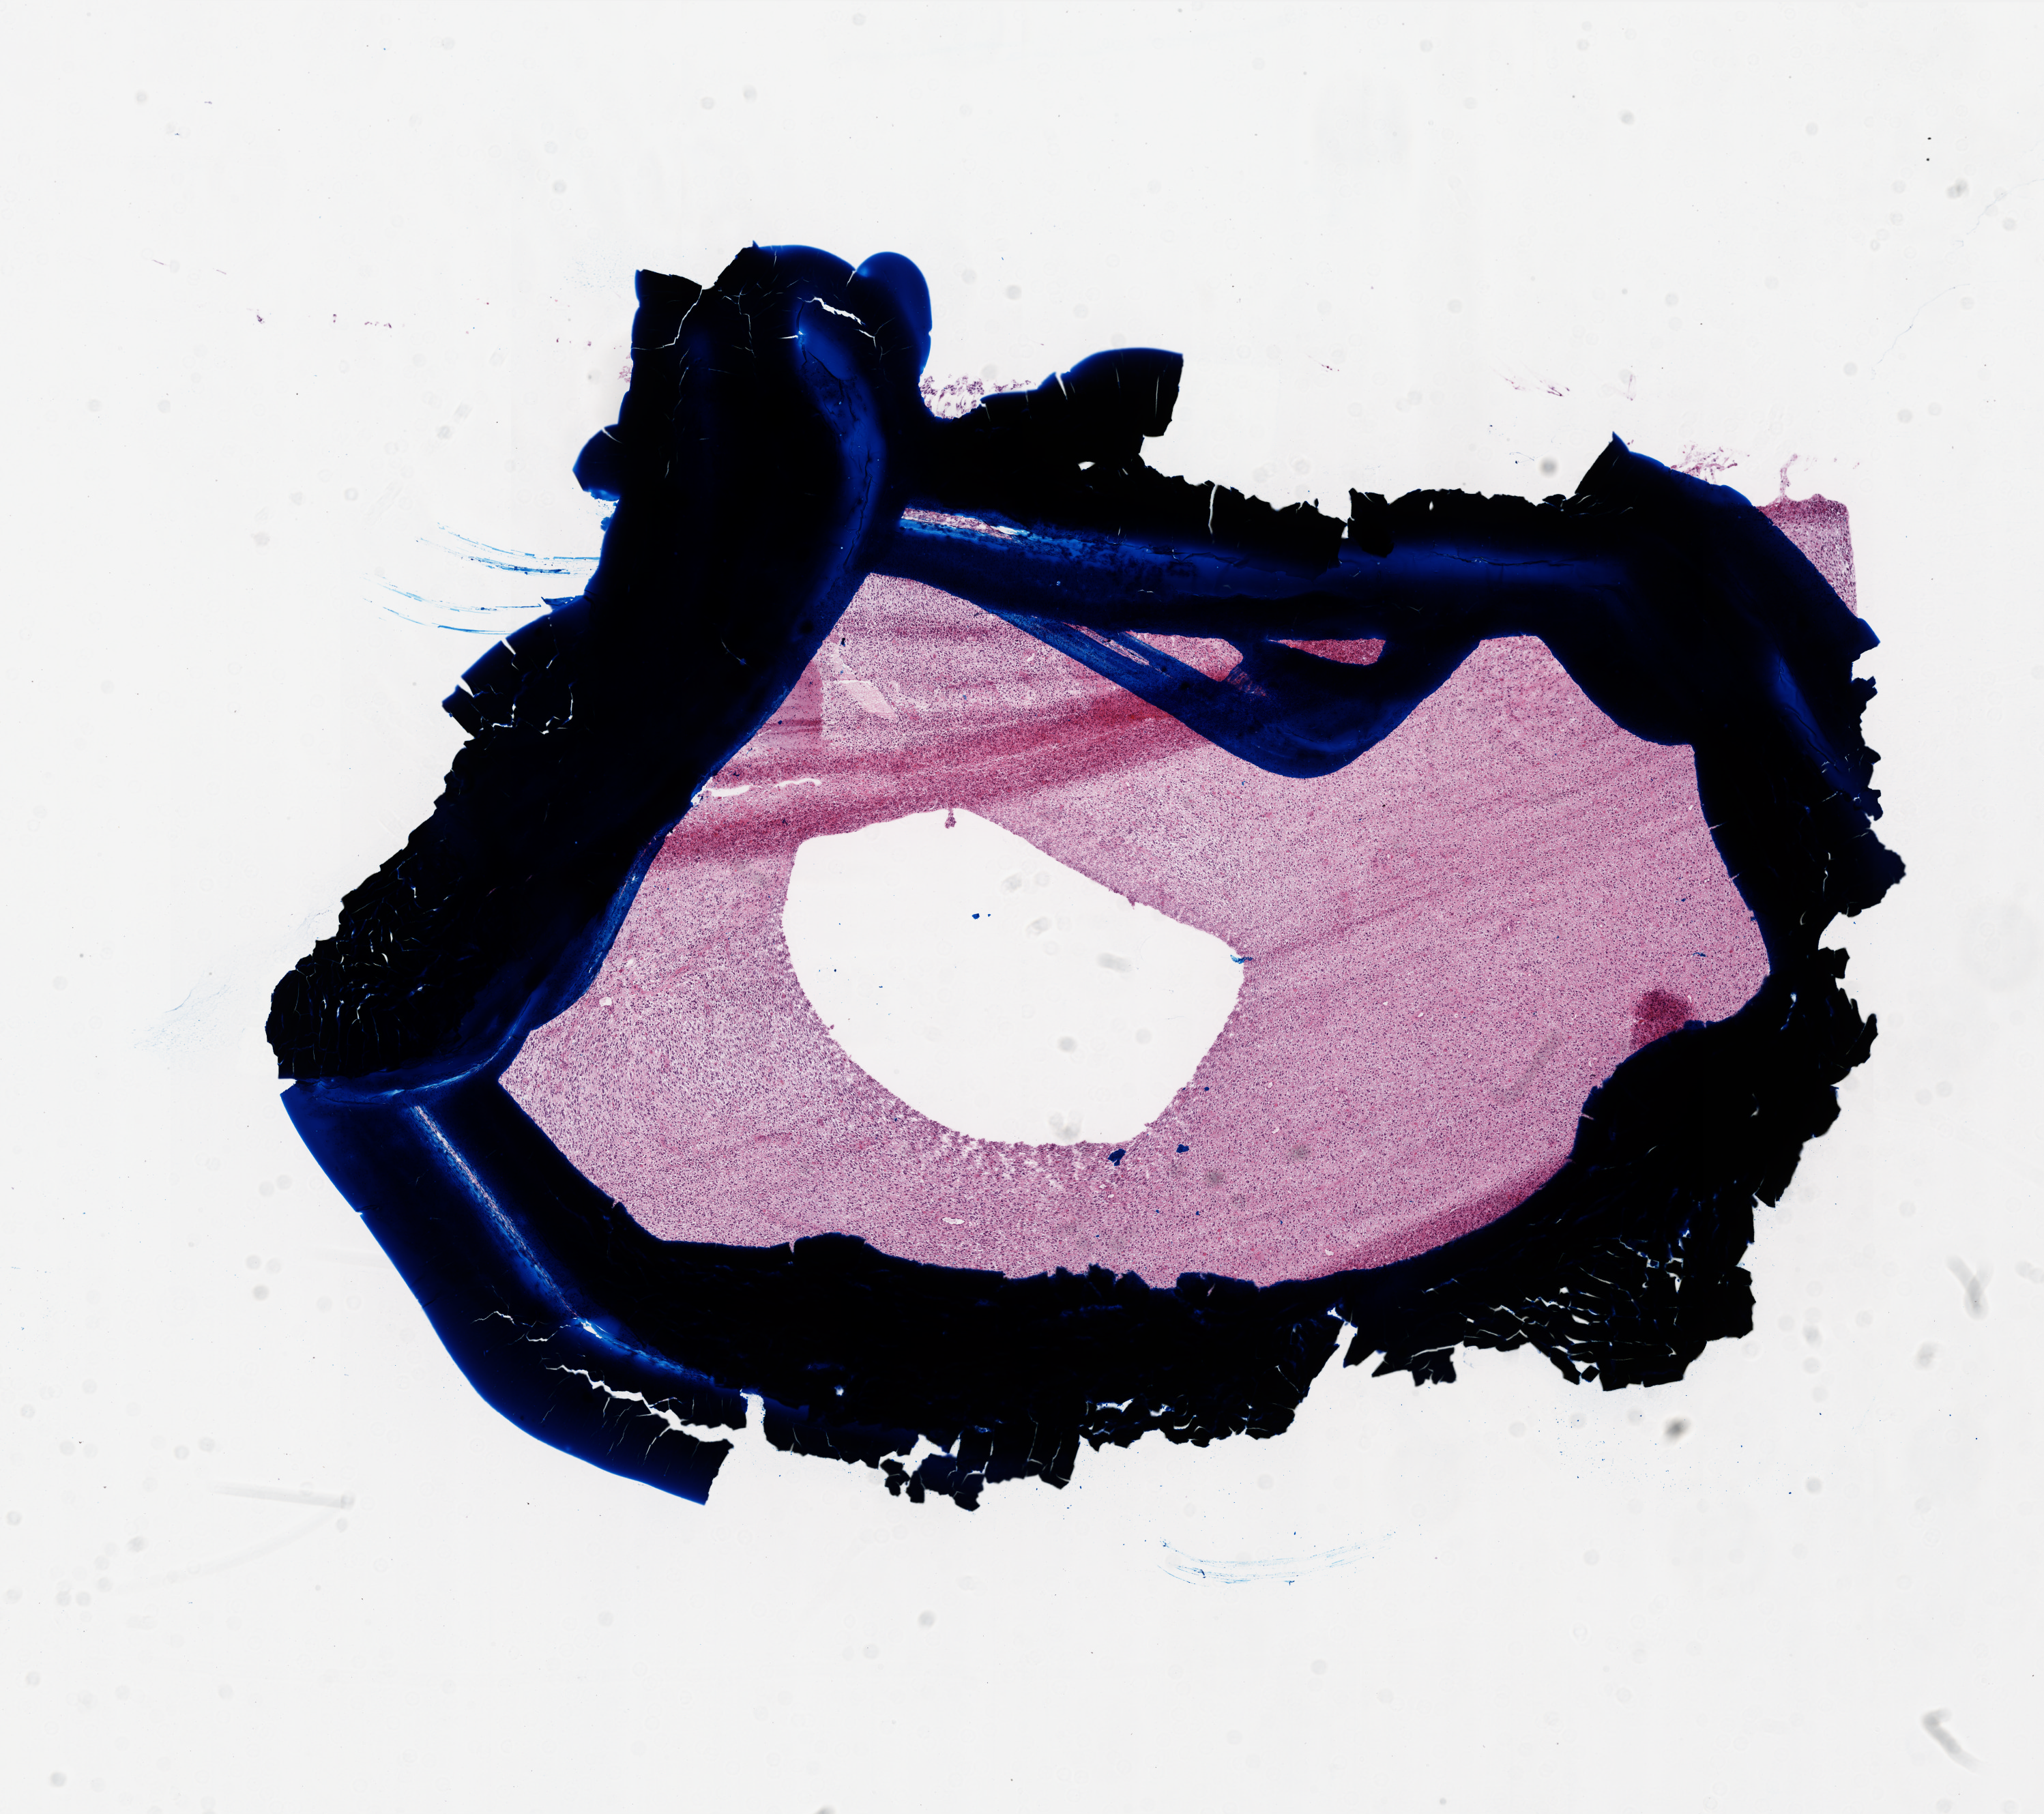
Digitized Hematoxylin and eosin (H&E) stained tissue section (whole slide), shown as a low-resolution overview of the whole scanned area (about 12.0 x 10.6 mm). Frozen section from the top of the tissue portion. Sample: primary tumour, brain. Patient: male, age at initial diagnosis 38 years. Slide review estimates, as recorded: tumour cells 100%, tumour nuclei 100%, normal cells 0%, stromal cells 0%, necrosis 0%.
* diagnosis: Glioblastoma